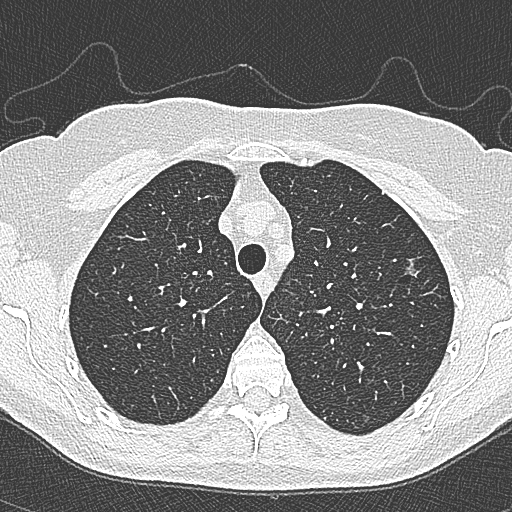
Low-dose screening chest CT, axial slice, second screening round (one year after baseline), lung window (W 1500 / L -600 HU), 120 kVp, slice 73 of 350 in the series. Female, age 65 years at enrolment. Current smoker at enrolment.
Lesion marked by an expert reader, bounding box <394,251,432,290> (left, top, right, bottom; pixels). The screening reader recorded 4 non-calcified nodules or masses ≥4 mm on this exam; which of them this box marks is not recorded. Official screen result: positive, change unspecified: nodule(s) >= 4 mm or enlarging nodule(s), mass(es), or other non-specific abnormalities suspicious for lung cancer. Later outcome: lung cancer diagnosed 54 days after this screen — bronchiolo-alveolar carcinoma, non-mucinous, left upper lobe, stage IA (AJCC 6th edition), 10 mm at pathology.